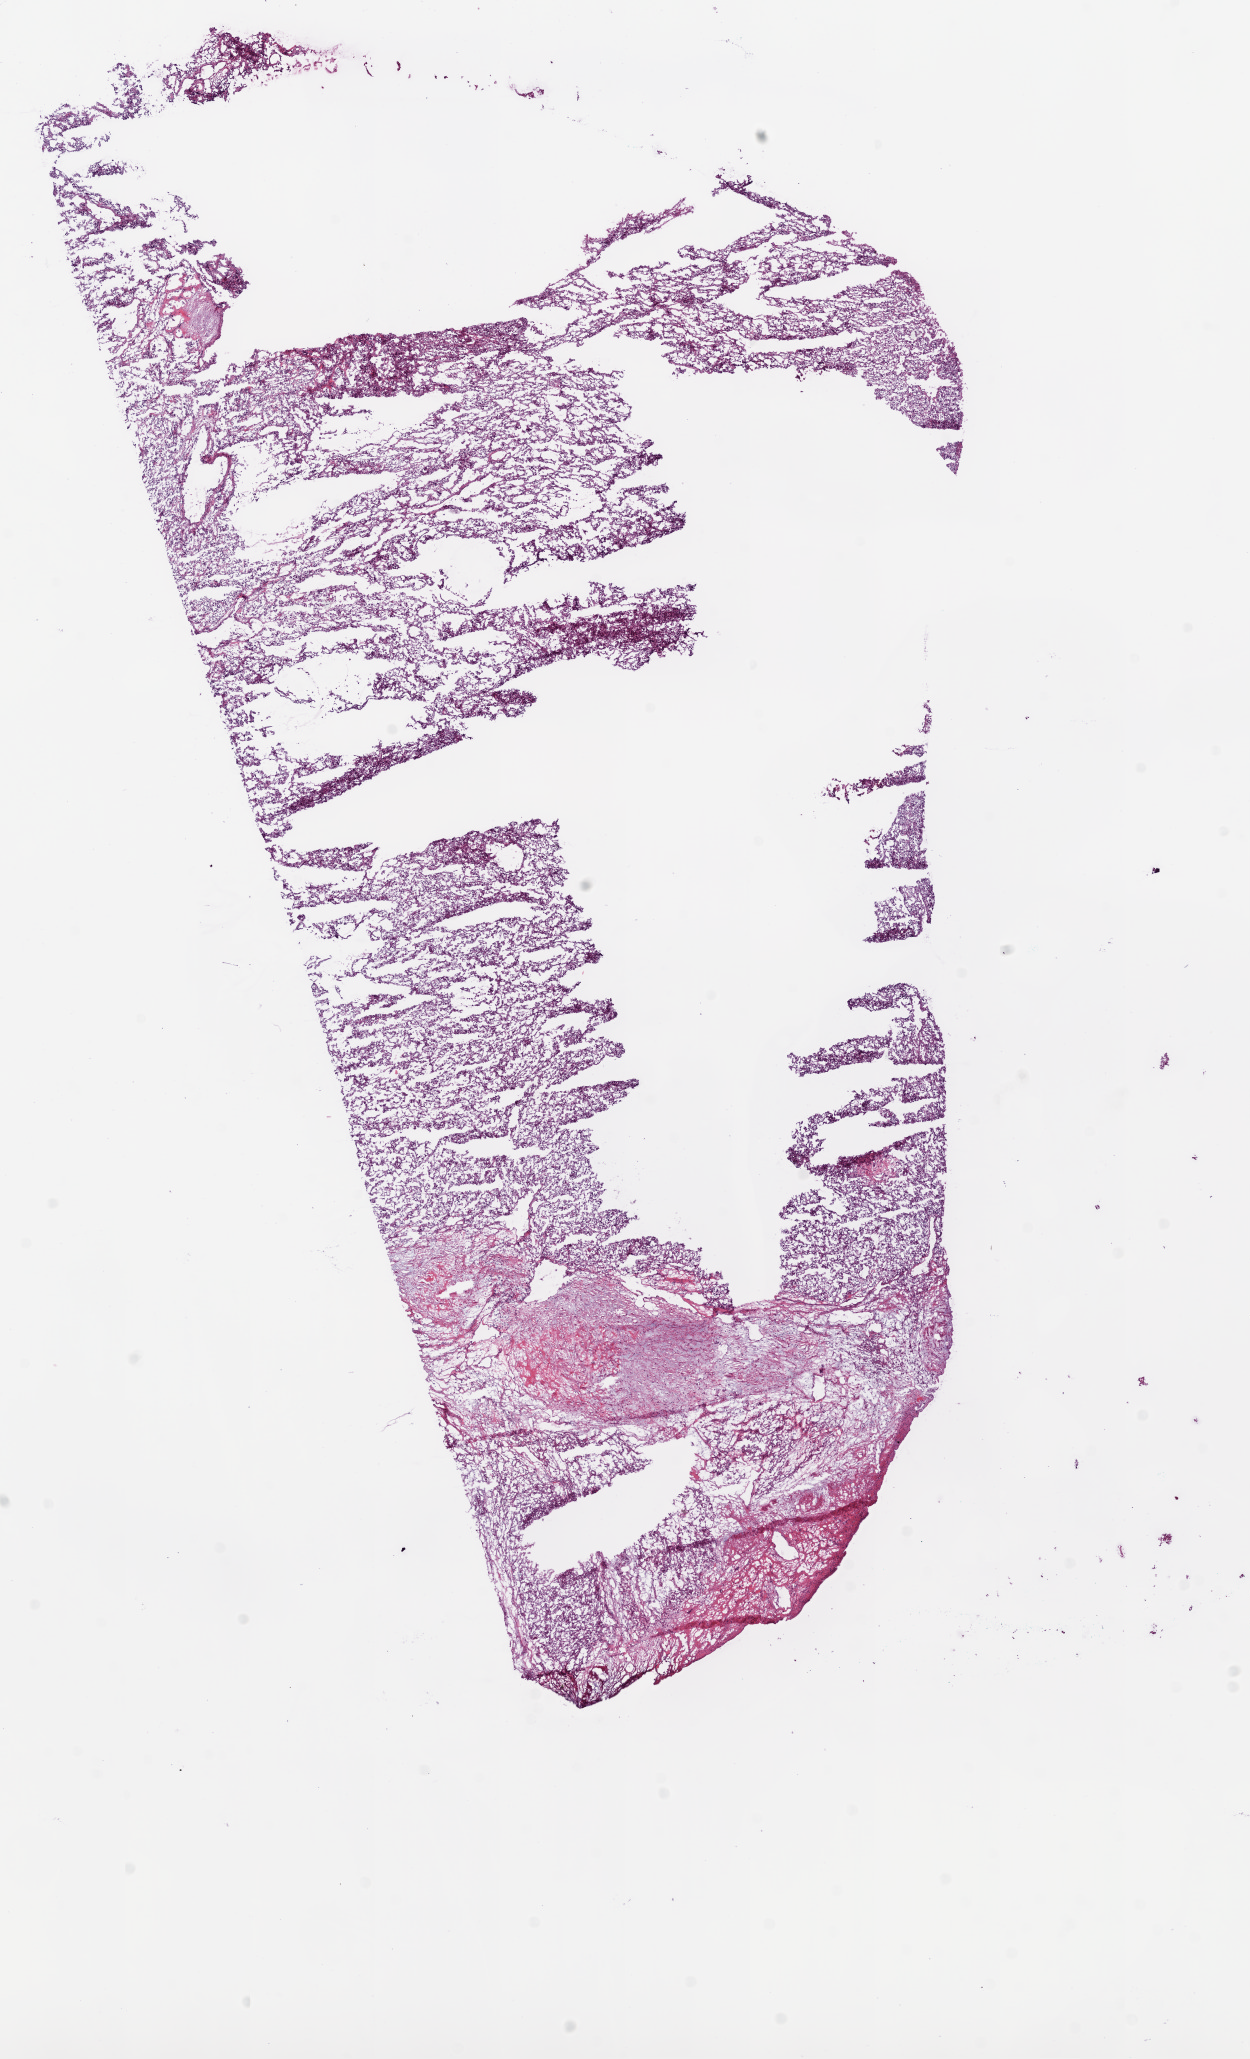
H&E whole-slide image — low-resolution overview of the scanned area, about 10.0 x 16.5 mm. Frozen section. Primary tumour sample from the kidney. Patient: male, age at initial diagnosis 69 years. Histologic grade: G3 (poorly differentiated). Pathologist review of this section (percent, as recorded): tumour cells 90%, tumour nuclei 80%, normal cells 0%, stromal cells 10%, necrosis 0%.
- histologic diagnosis: Clear cell adenocarcinoma, NOS
- AJCC pathologic stage: III (6th edition)